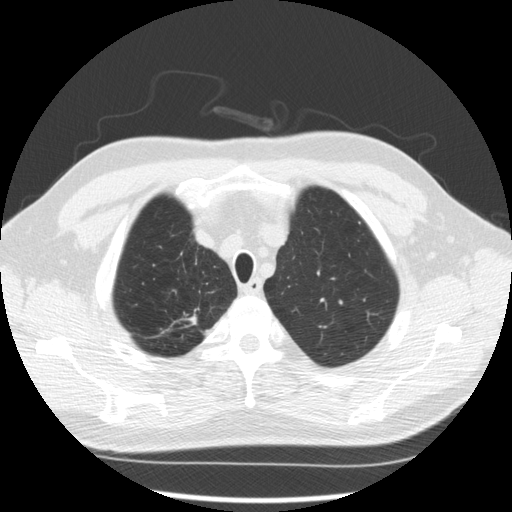
Chest CT (low-dose screening protocol), one axial image, second screening round (one year after baseline), lung window (W 1500 / L -600 HU), slice 41 of 289 in the series. Male participant, aged 64 years at enrolment. Former smoker at enrolment.
Expert-annotated lung lesion, bounding box [x1, y1, x2, y2] px = [174, 301, 213, 338]. The screening reader recorded 3 non-calcified nodules or masses ≥4 mm on this exam; which of them this box marks is not recorded. Participant outcome: lung cancer diagnosed 411 days after this screen (after the third annual screen) — adenocarcinoma, NOS, right upper lobe, moderately differentiated (G2), stage IA (AJCC 6th edition), 14 mm at pathology.